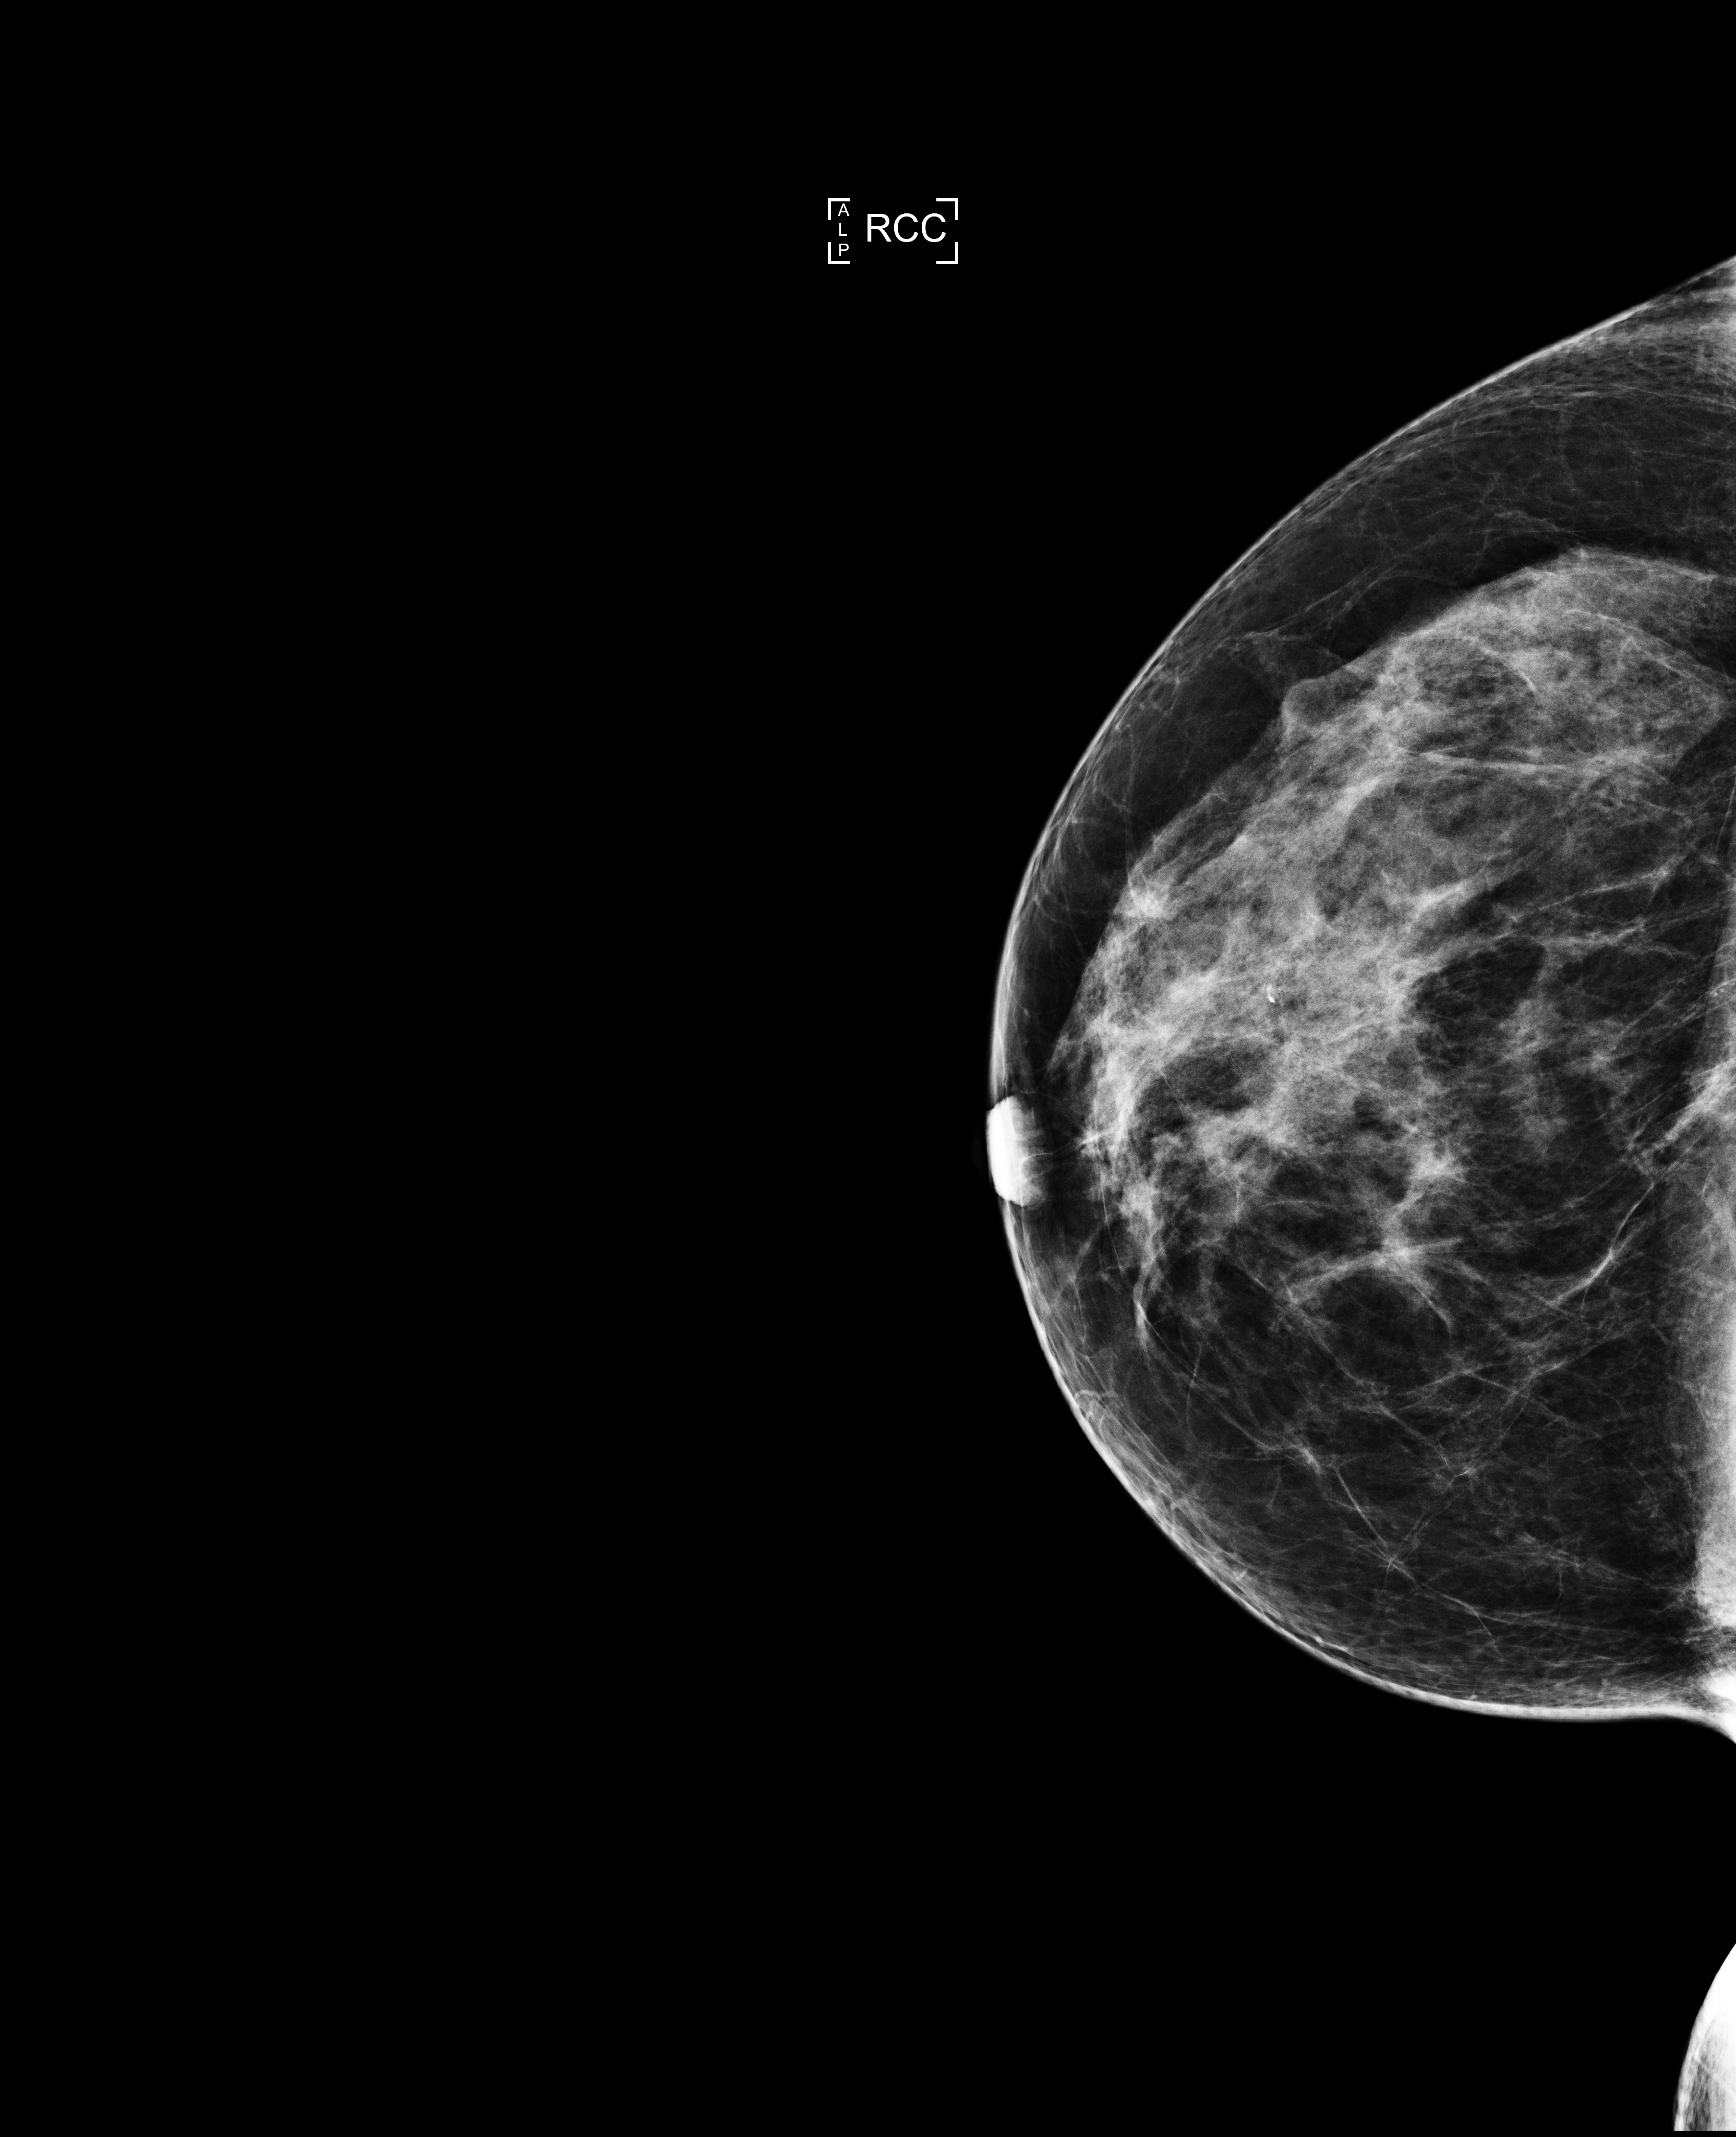
Full-field digital mammogram (FFDM), right breast, cranio-caudal projection, screening examination. Patient aged 57 years (female).
- breast density at the screening exam (both breasts): heterogeneously dense (BI-RADS density category c)
- final BI-RADS assessment for this screening round (tomosynthesis exam, both breasts): category 1
- recall: no recall after this screen